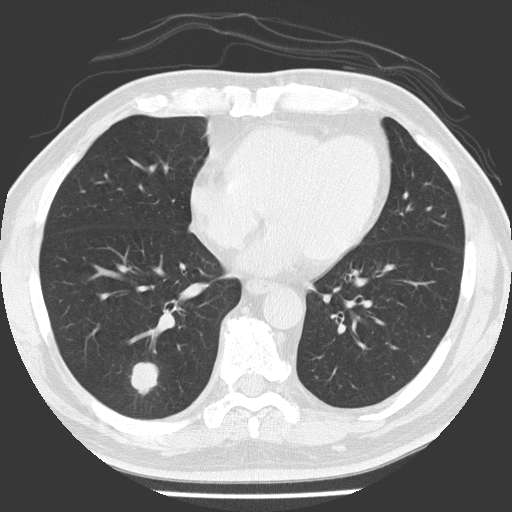
Low-dose screening chest CT, one axial slice. Position 63 of 154 along the scan axis. Reconstruction kernel FC51. 120 kVp. Lung window (W 1500 / L -600 HU). 2 mm slice thickness. 512 × 512 image matrix.
Outlined on this slice (expert manual segmentation):
- lesion 1 (tumor, lower lobe of right lung): box from (x=131, y=362) to (x=158, y=395) px